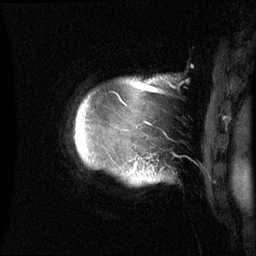
Breast MRI (dynamic contrast-enhanced), one sagittal slice. Slice 57 of 60 in the series (ordered by position). Dynamic contrast-enhanced series, image 2 of 3 at this slice position (ordered by acquisition). 1.5 T. TE 4.2 ms, TR 8.4 ms. 256 × 256 image matrix. Patient: female, 48 years.
Outlined on this slice (semi-automatic segmentation, software-assisted and operator-edited):
- analysis volume of interest (the breast-tissue region the enhancement analysis was run in; not a lesion): bounding box <75,78,166,184> (left, top, right, bottom; pixels)
- tumour enhancement mask (voxels above the 70 % enhancement threshold inside the analysis volume of interest): <133,82,145,169>